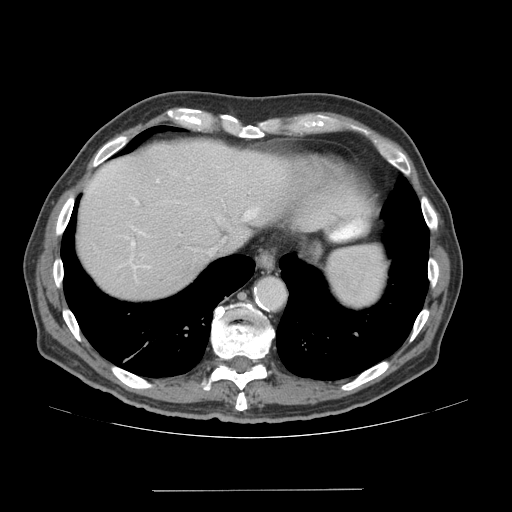
Contrast-enhanced abdominal CT (liver protocol), one axial slice. Slice 59 of 77 in the series (ordered by position). Reconstruction kernel STANDARD. Soft-tissue window (W 400 / L 40 HU). 2.5 mm slice thickness. 512 × 512 image matrix. Case-level facts recorded for this patient, not image findings: diagnosis: hepatocellular carcinoma (patient treated with transarterial chemoembolisation; whether this scan precedes or follows treatment is not stated here); TNM stage (as recorded): Stage-IVA; Child-Pugh class: A; tumour differentiation: well differentiated; tumour nodularity: uninodular.
Annotated regions visible in this slice (semi-automatically segmented with operator editing):
- abdominal aorta: bounding box [x1, y1, x2, y2] px = [256, 280, 285, 308]
- liver parenchyma outside the tumour (the mass and vessels are separate outlines, so this box may not span the whole liver): [78, 140, 368, 298]
- liver vessels: [93, 166, 258, 277]